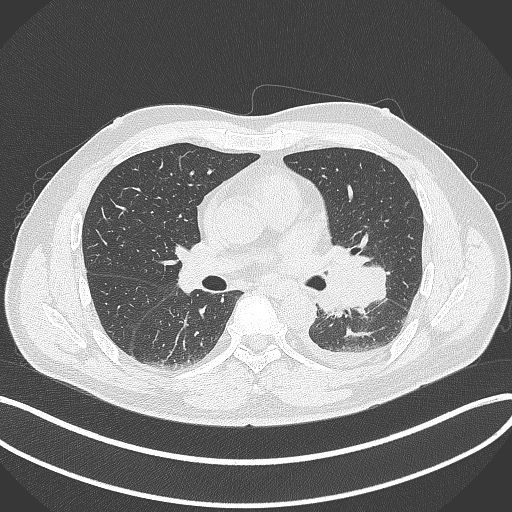
Chest CT, one axial slice; position 194 of 342 along the scan axis; lung window (W 1500 / L -600 HU); 1 mm slice thickness; 512 × 512 image matrix, field of view 400 × 400 mm. Patient: male, 58 years. From the clinical record (not read from this slice): clinical TNM (as recorded): T3 N1 M1b; histopathological grade: G3.
Structures marked on this image (bounding box drawn by a radiologist):
- lung tumour (recorded histology: small cell carcinoma): bounding box (x1, y1, x2, y2) in pixels: (316, 246, 390, 320)